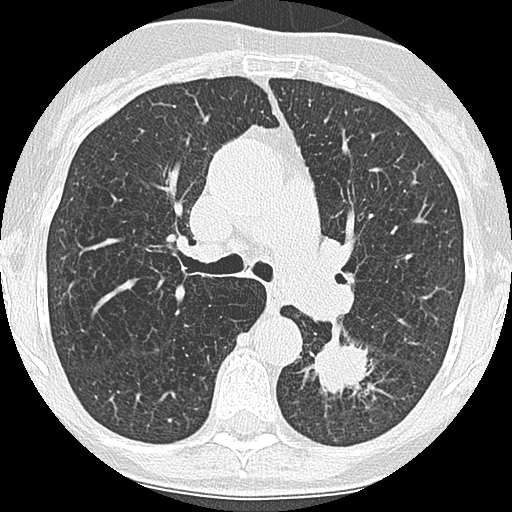
Low-dose screening chest CT, one axial slice; slice 112 of 171 in the series (ordered by position); reconstruction kernel LUNG; 120 kVp; lung window (W 1500 / L -600 HU); 2.5 mm slice thickness; 512 × 512 image matrix, field of view 280 × 280 mm.
Outlined on this slice (expert manual segmentation):
- lesion 1 (tumor, lower lobe of left lung): bounding box <312,335,372,394> (left, top, right, bottom; pixels)